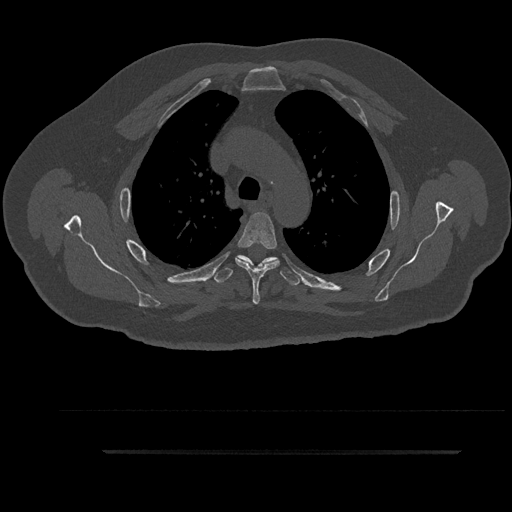
CT including the spine, one axial slice. Slice 661 of 797 in the series (ordered by position). Reconstruction kernel Br40s/3. 120 kVp. Bone window (W 1800 / L 400 HU). 512 × 512 image matrix, field of view 432 × 432 mm. Patient: male, 63 years. From the clinical record (not read from this slice): primary cancer: renal; vertebrae with lytic lesions (as recorded): T8.
Outlined on this slice (semi-automatic segmentation, software-assisted and operator-edited):
- T4 vertebra: box from (x=235, y=212) to (x=280, y=305) px
- T5 vertebra: (x=213, y=255)–(x=300, y=286)